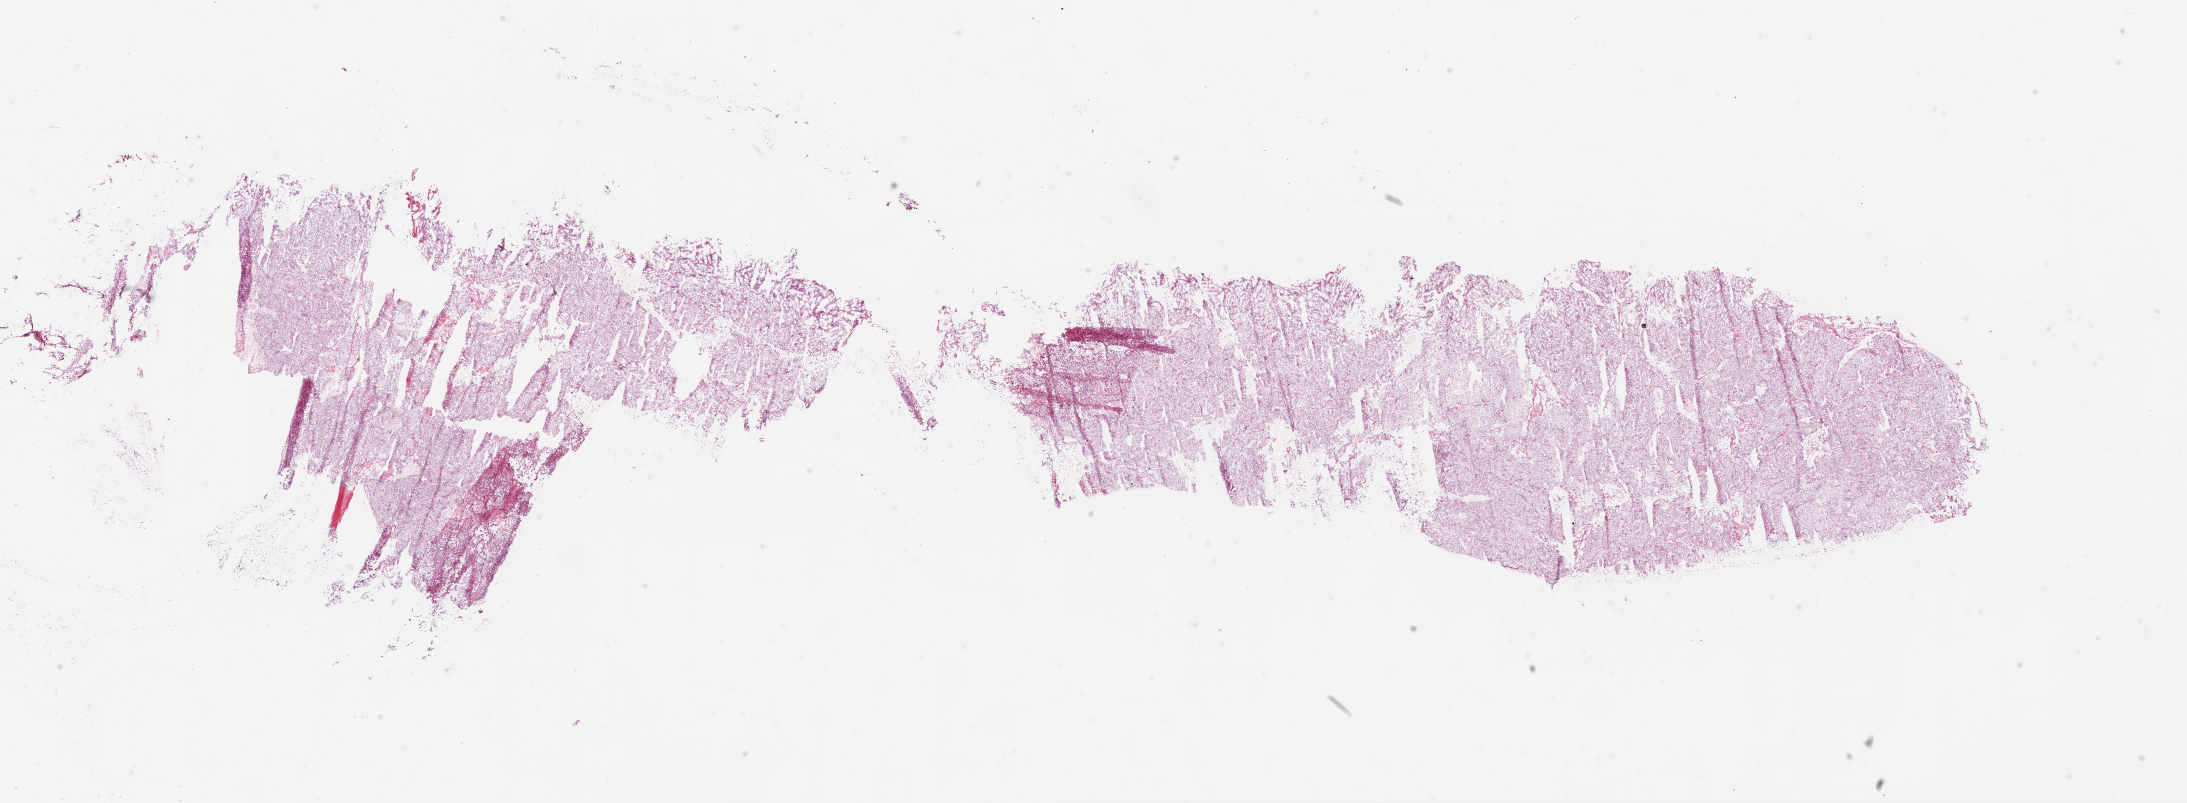
Digitized H&E-stained tissue section (whole slide), a low-resolution overview of the entire scanned area, about 35.1 x 12.9 mm, frozen section, kidney, primary tumour sample. Male, age 48 years at initial diagnosis. Histologic grade: G3 (poorly differentiated). Composition of this section per pathologist review: tumour cells 90%, tumour nuclei 85%, normal cells 0%, stromal cells 10%, necrosis 0%.
- pathologic diagnosis: Clear cell adenocarcinoma, NOS
- TNM: T1b NX M0
- AJCC pathologic stage: I